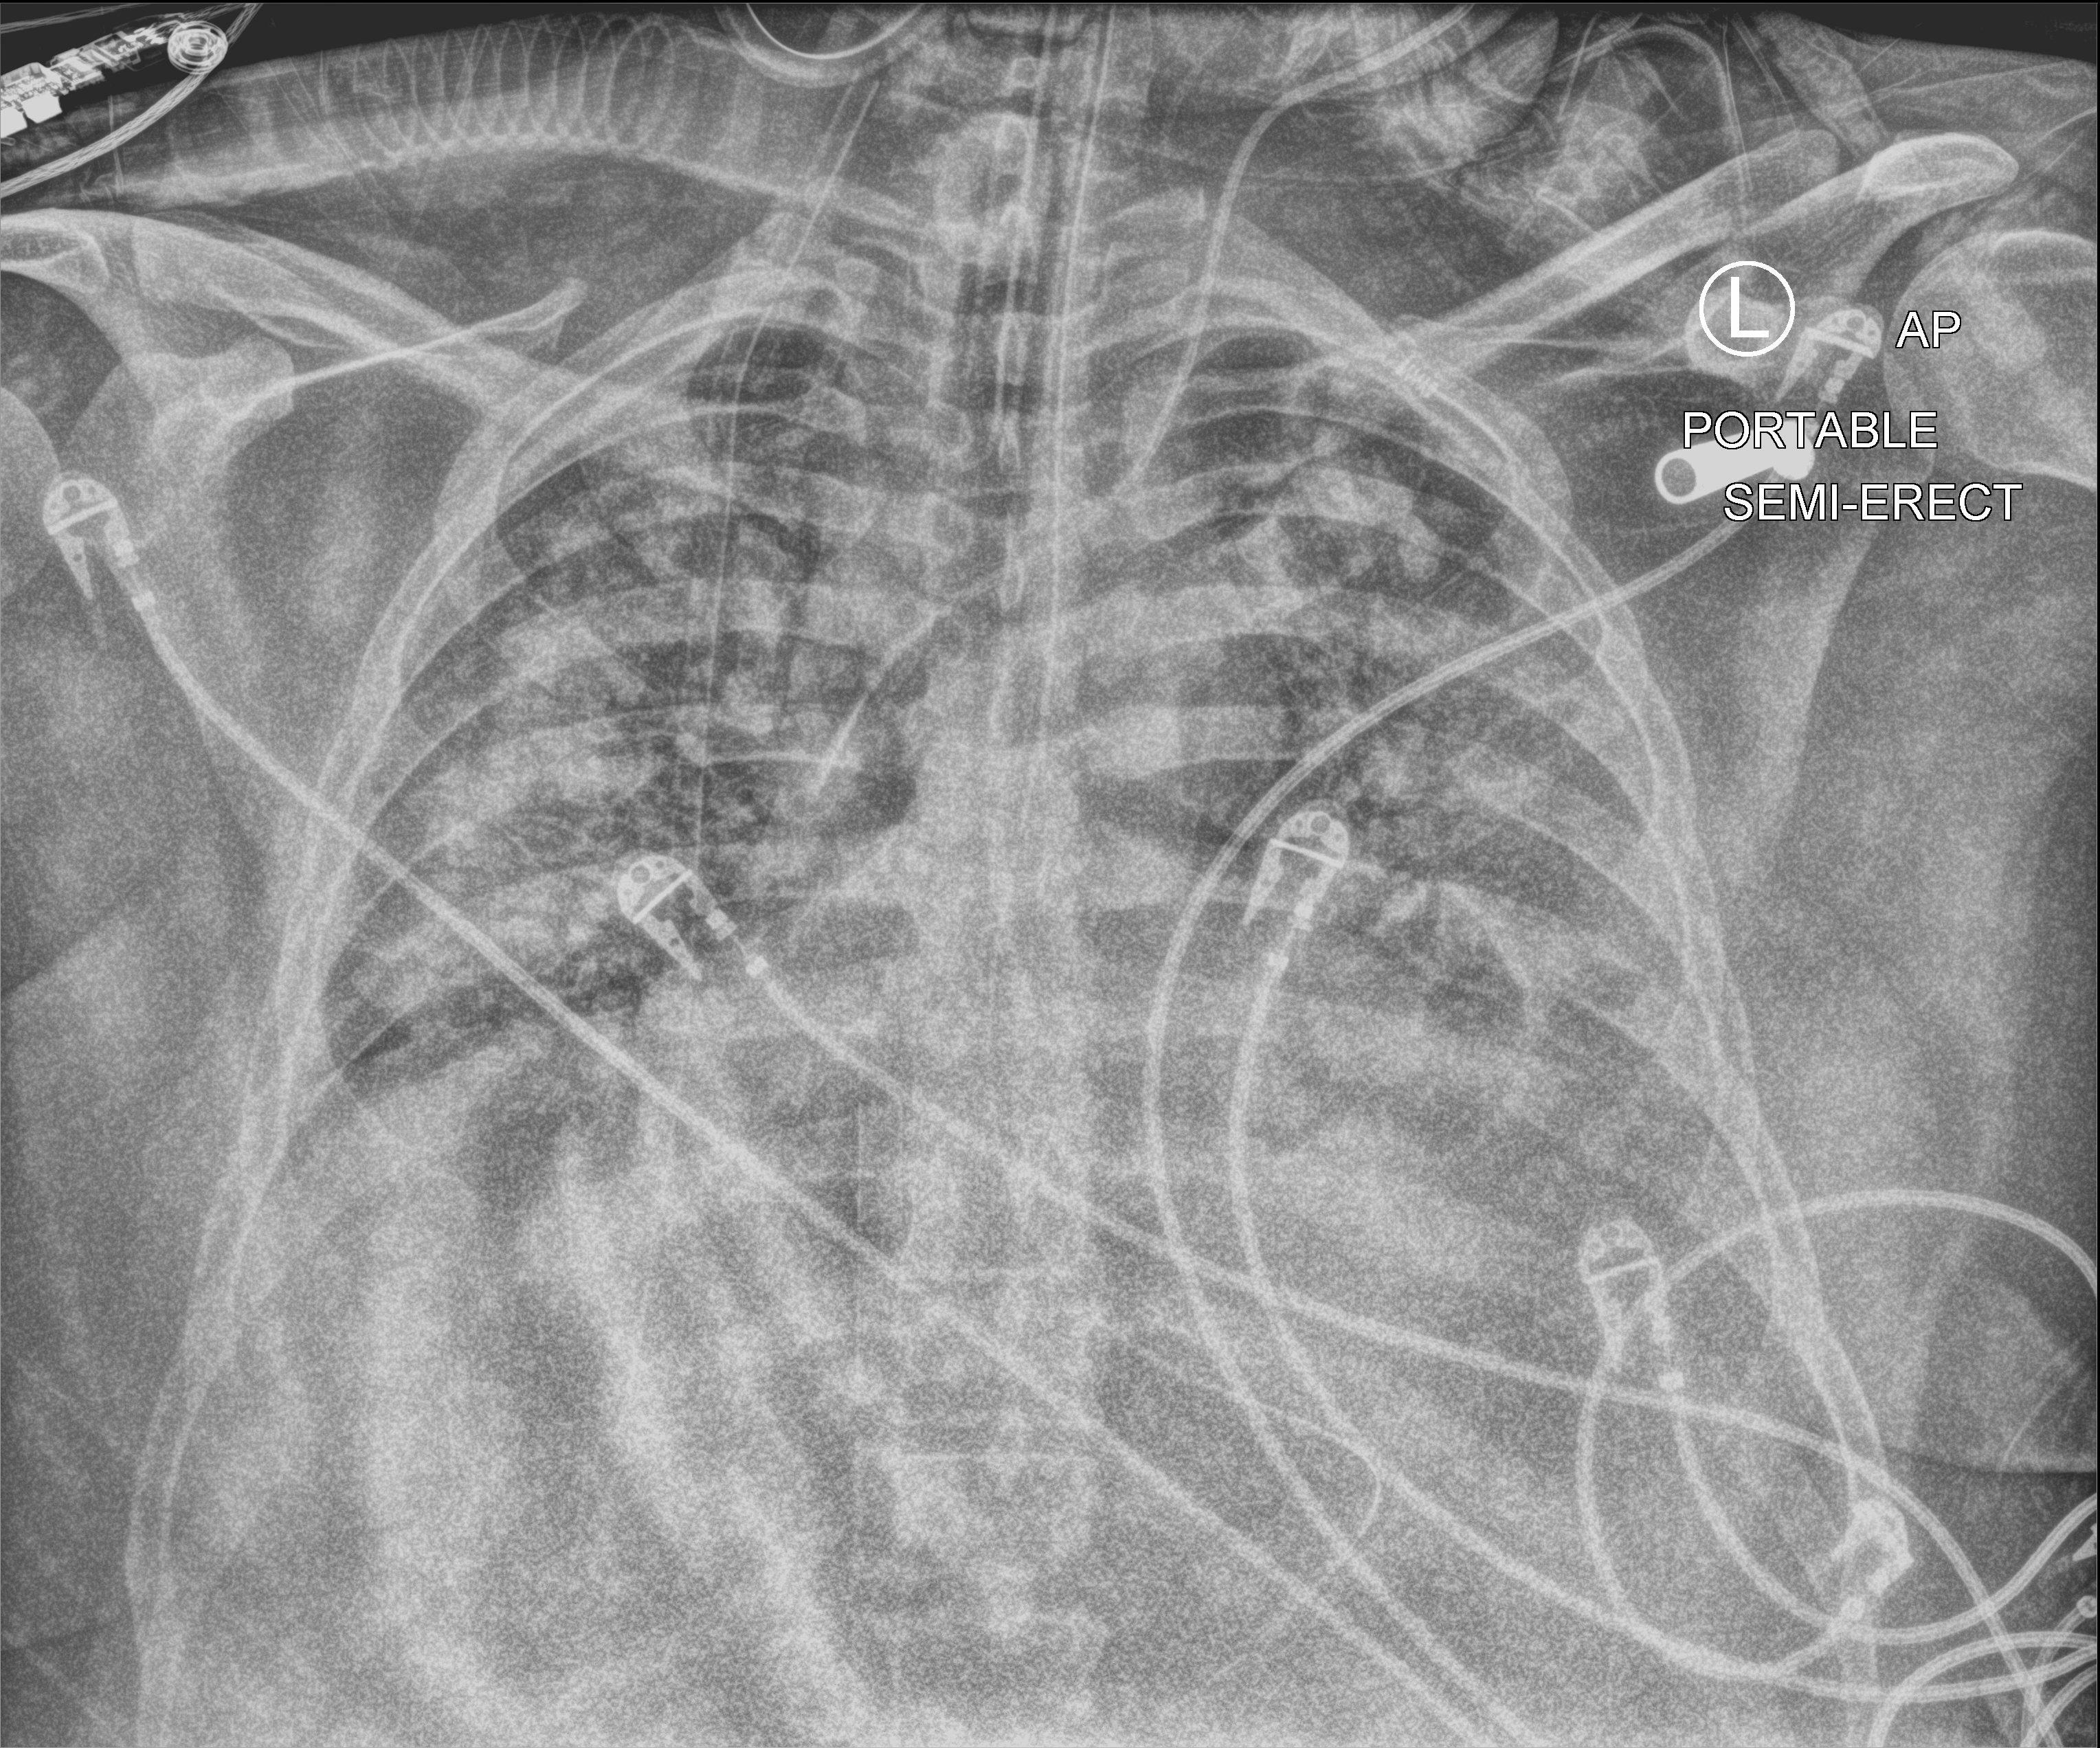
Portable chest radiograph, anteroposterior (AP) projection. Adult patient hospitalised with COVID-19, age 18–59 years.
Admission-level facts for this patient (not findings on this image; timing relative to this image not recorded): mechanically ventilated during this hospital stay: yes; other chronic lung disease (admission record): no.